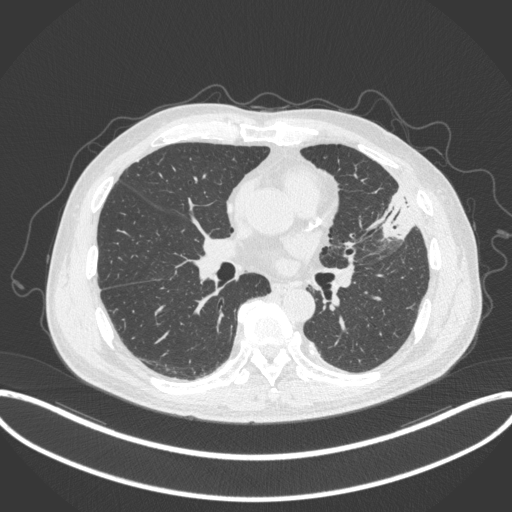
Chest CT, one axial slice; position 167 of 382 along the scan axis; reconstruction kernel B31f; lung window (W 1500 / L -600 HU); 1 mm slice thickness; 512 × 512 image matrix. Male patient, age 64 years. From the clinical record (not read from this slice): clinical TNM (as recorded): T4 N1 M0.
Annotated regions visible in this slice (rectangle marked by the reading radiologist):
- lung tumour (recorded histology: adenocarcinoma): bounding box [x1, y1, x2, y2] px = [369, 183, 415, 244]